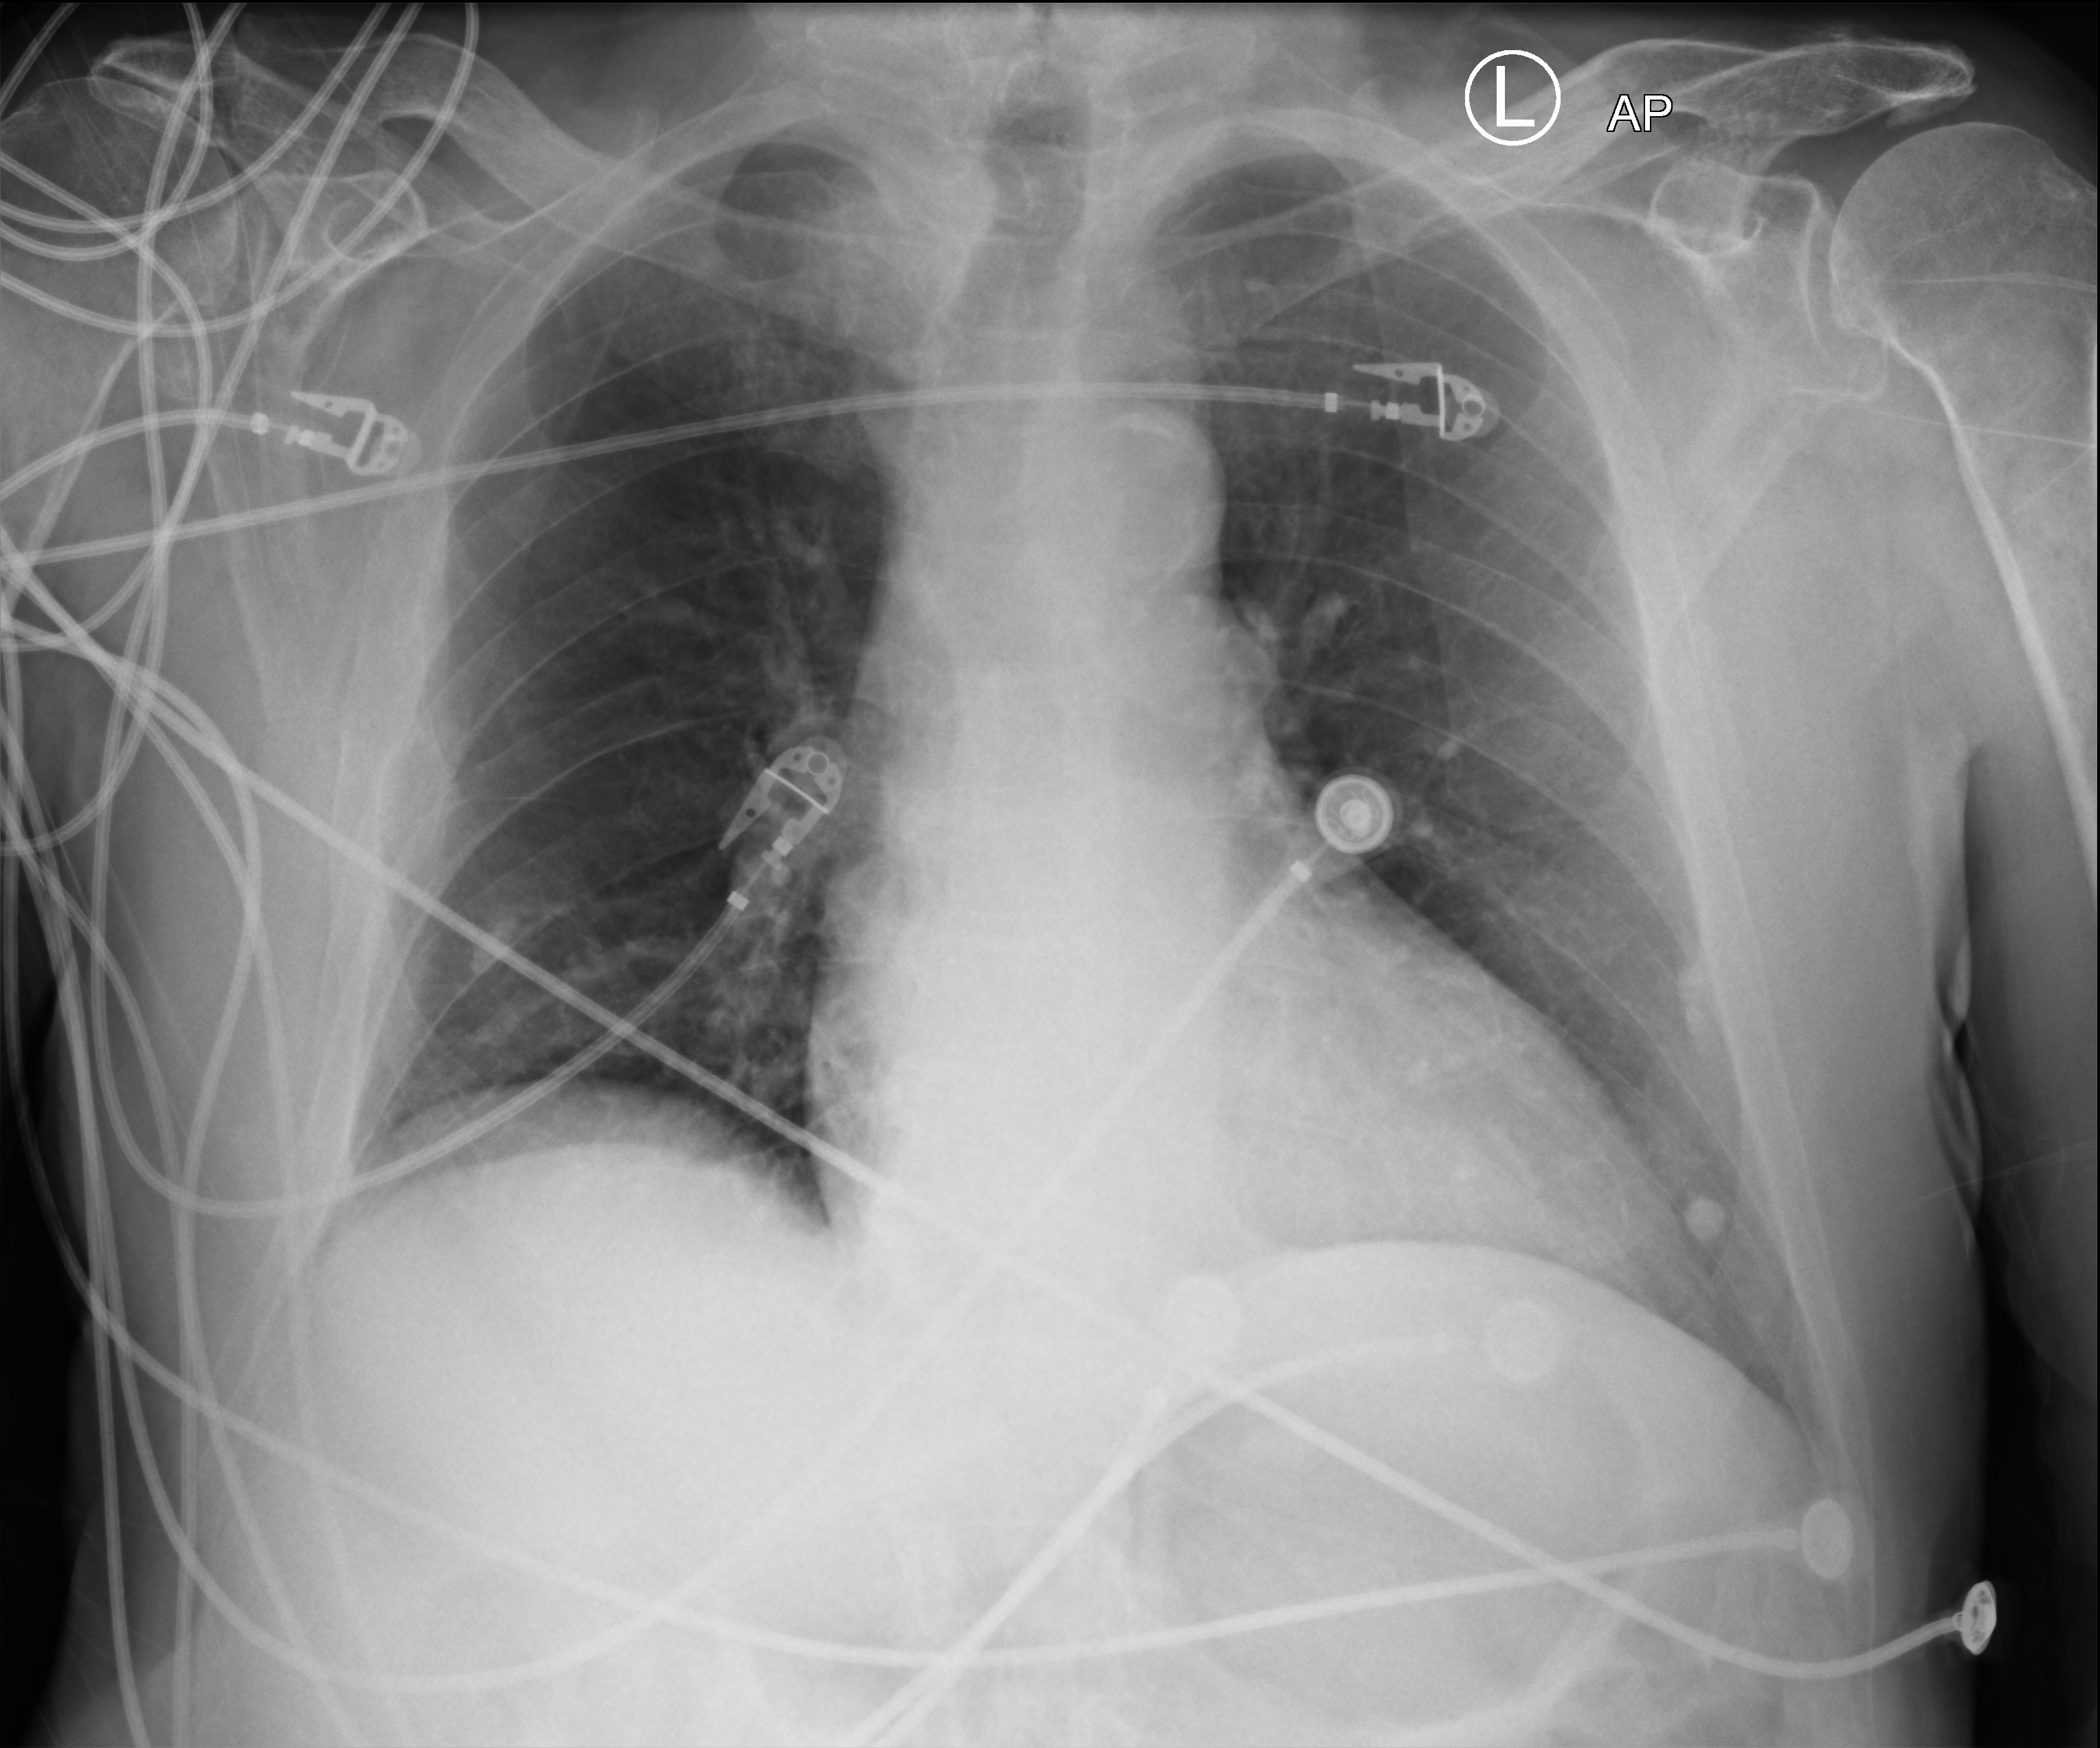
Chest X-ray (portable); anteroposterior (AP) projection. Patient hospitalised with COVID-19; male, aged 75–90 years.
Hospital-stay facts (about this admission, not read from this image; timing relative to this image not recorded):
- admitted to intensive care during this hospital stay: no
- mechanically ventilated during this hospital stay: no